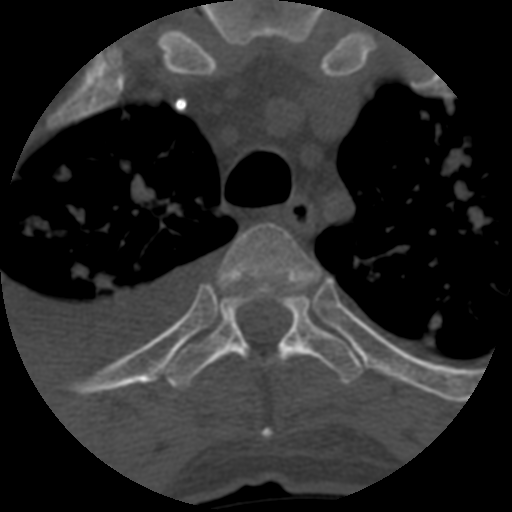
CT including the spine, one axial slice. Position 478 of 708 along the scan axis. 120 kVp. One of 3 acquisitions stored at this slice position. Bone window (W 1800 / L 400 HU). 1.25 mm slice thickness. 512 × 512 image matrix, field of view 160 × 160 mm. Patient age 55 years. Case-level facts recorded for this patient, not image findings: primary cancer: colon.
Outlined on this slice (semi-automatically segmented with operator editing):
- T3 vertebra: bounding box <219,224,319,437> (left, top, right, bottom; pixels)
- T4 vertebra: <164,284,365,389>